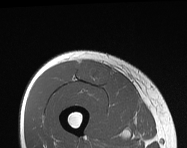
MRI of an extremity soft-tissue mass, one axial slice; position 50 of 114 along the scan axis; MR volume resampled by the dataset authors to the PET/CT grid (not the native acquisition matrix); 3.27 mm slice thickness; 187 × 148 image matrix, field of view 183 × 145 mm. Male patient. From the clinical record (not read from this slice): histological type: pleiomorphic leiomyosarcoma; grade: intermediate; site of the primary tumour: right thigh.
Structures marked on this image (expert contour drawn on MRI and transferred to this co-registered scan by the dataset authors):
- gross tumour volume including surrounding oedema: bounding box (x1, y1, x2, y2) in pixels: (77, 61, 112, 87)